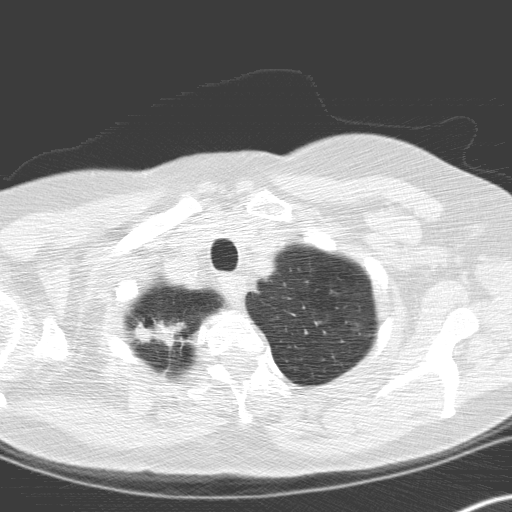
Low-dose screening chest CT, one axial slice; slice 144 of 166 in the series (ordered by position); lung window (W 1500 / L -600 HU); 3.2 mm slice thickness; 512 × 512 image matrix, field of view 306 × 306 mm.
Outlined on this slice (manually delineated by an expert):
- lesion 1 (tumor, upper lobe of right lung): box from (x=136, y=321) to (x=176, y=344) px